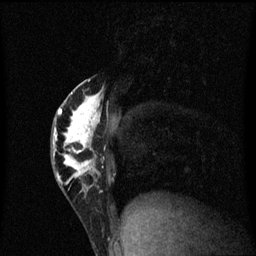
Breast MRI (dynamic contrast-enhanced), one sagittal slice; position 27 of 60 along the scan axis; dynamic contrast-enhanced series, image 2 of 3 at this slice position (ordered by acquisition); 1.5 T; TE 4.2 ms, TR 8.4 ms; 2 mm slice thickness; 256 × 256 image matrix, field of view 200 × 200 mm. Female patient, age 40 years.
Structures marked on this image (semi-automatically segmented with operator editing):
- analysis volume of interest (the breast-tissue region the enhancement analysis was run in; not a lesion): bounding box [x1, y1, x2, y2] px = [52, 74, 110, 203]
- tumour enhancement mask (voxels above the 70 % enhancement threshold inside the analysis volume of interest): [53, 80, 105, 193]